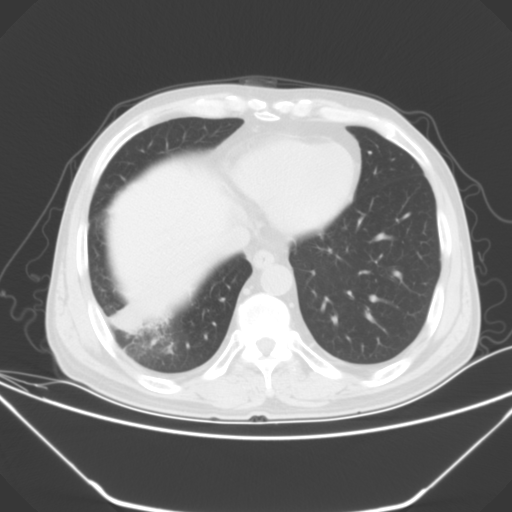
Chest CT, one axial slice. Slice 13 of 52 in the series (ordered by position). 120 kVp. Lung window (W 1500 / L -600 HU). 512 × 512 image matrix. Patient: male, 54 years. Case-level facts recorded for this patient, not image findings: clinical TNM (as recorded): T2 N1 M0.
Structures marked on this image (bounding box drawn by a radiologist):
- lung tumour (recorded histology: adenocarcinoma): bounding box <109,299,145,334> (left, top, right, bottom; pixels)